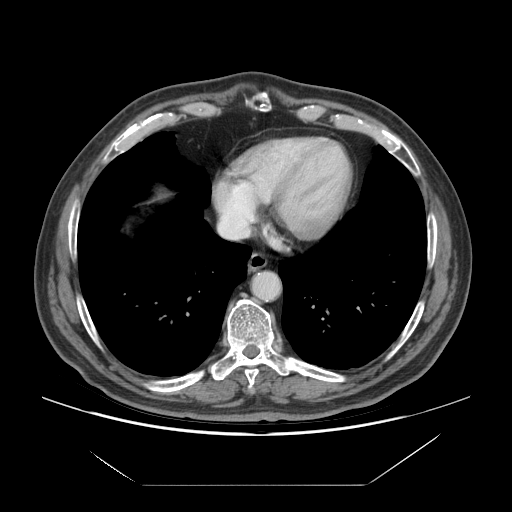
Contrast-enhanced abdominal CT (liver protocol), one axial slice; slice 69 of 75 in the series (ordered by position); reconstruction kernel STANDARD; 140 kVp; soft-tissue window (W 400 / L 40 HU); 2.5 mm slice thickness; 512 × 512 image matrix, field of view 420 × 420 mm. Case-level facts recorded for this patient, not image findings: diagnosis: hepatocellular carcinoma (patient treated with transarterial chemoembolisation; whether this scan precedes or follows treatment is not stated here); TNM stage (as recorded): Stage-I; Child-Pugh class: A; tumour nodularity: uninodular; tumour size: 5.8 cm.
Outlined on this slice (semi-automatically segmented with operator editing):
- liver parenchyma outside the tumour (the mass and vessels are separate outlines, so this box may not span the whole liver): bounding box <158,194,164,198> (left, top, right, bottom; pixels)